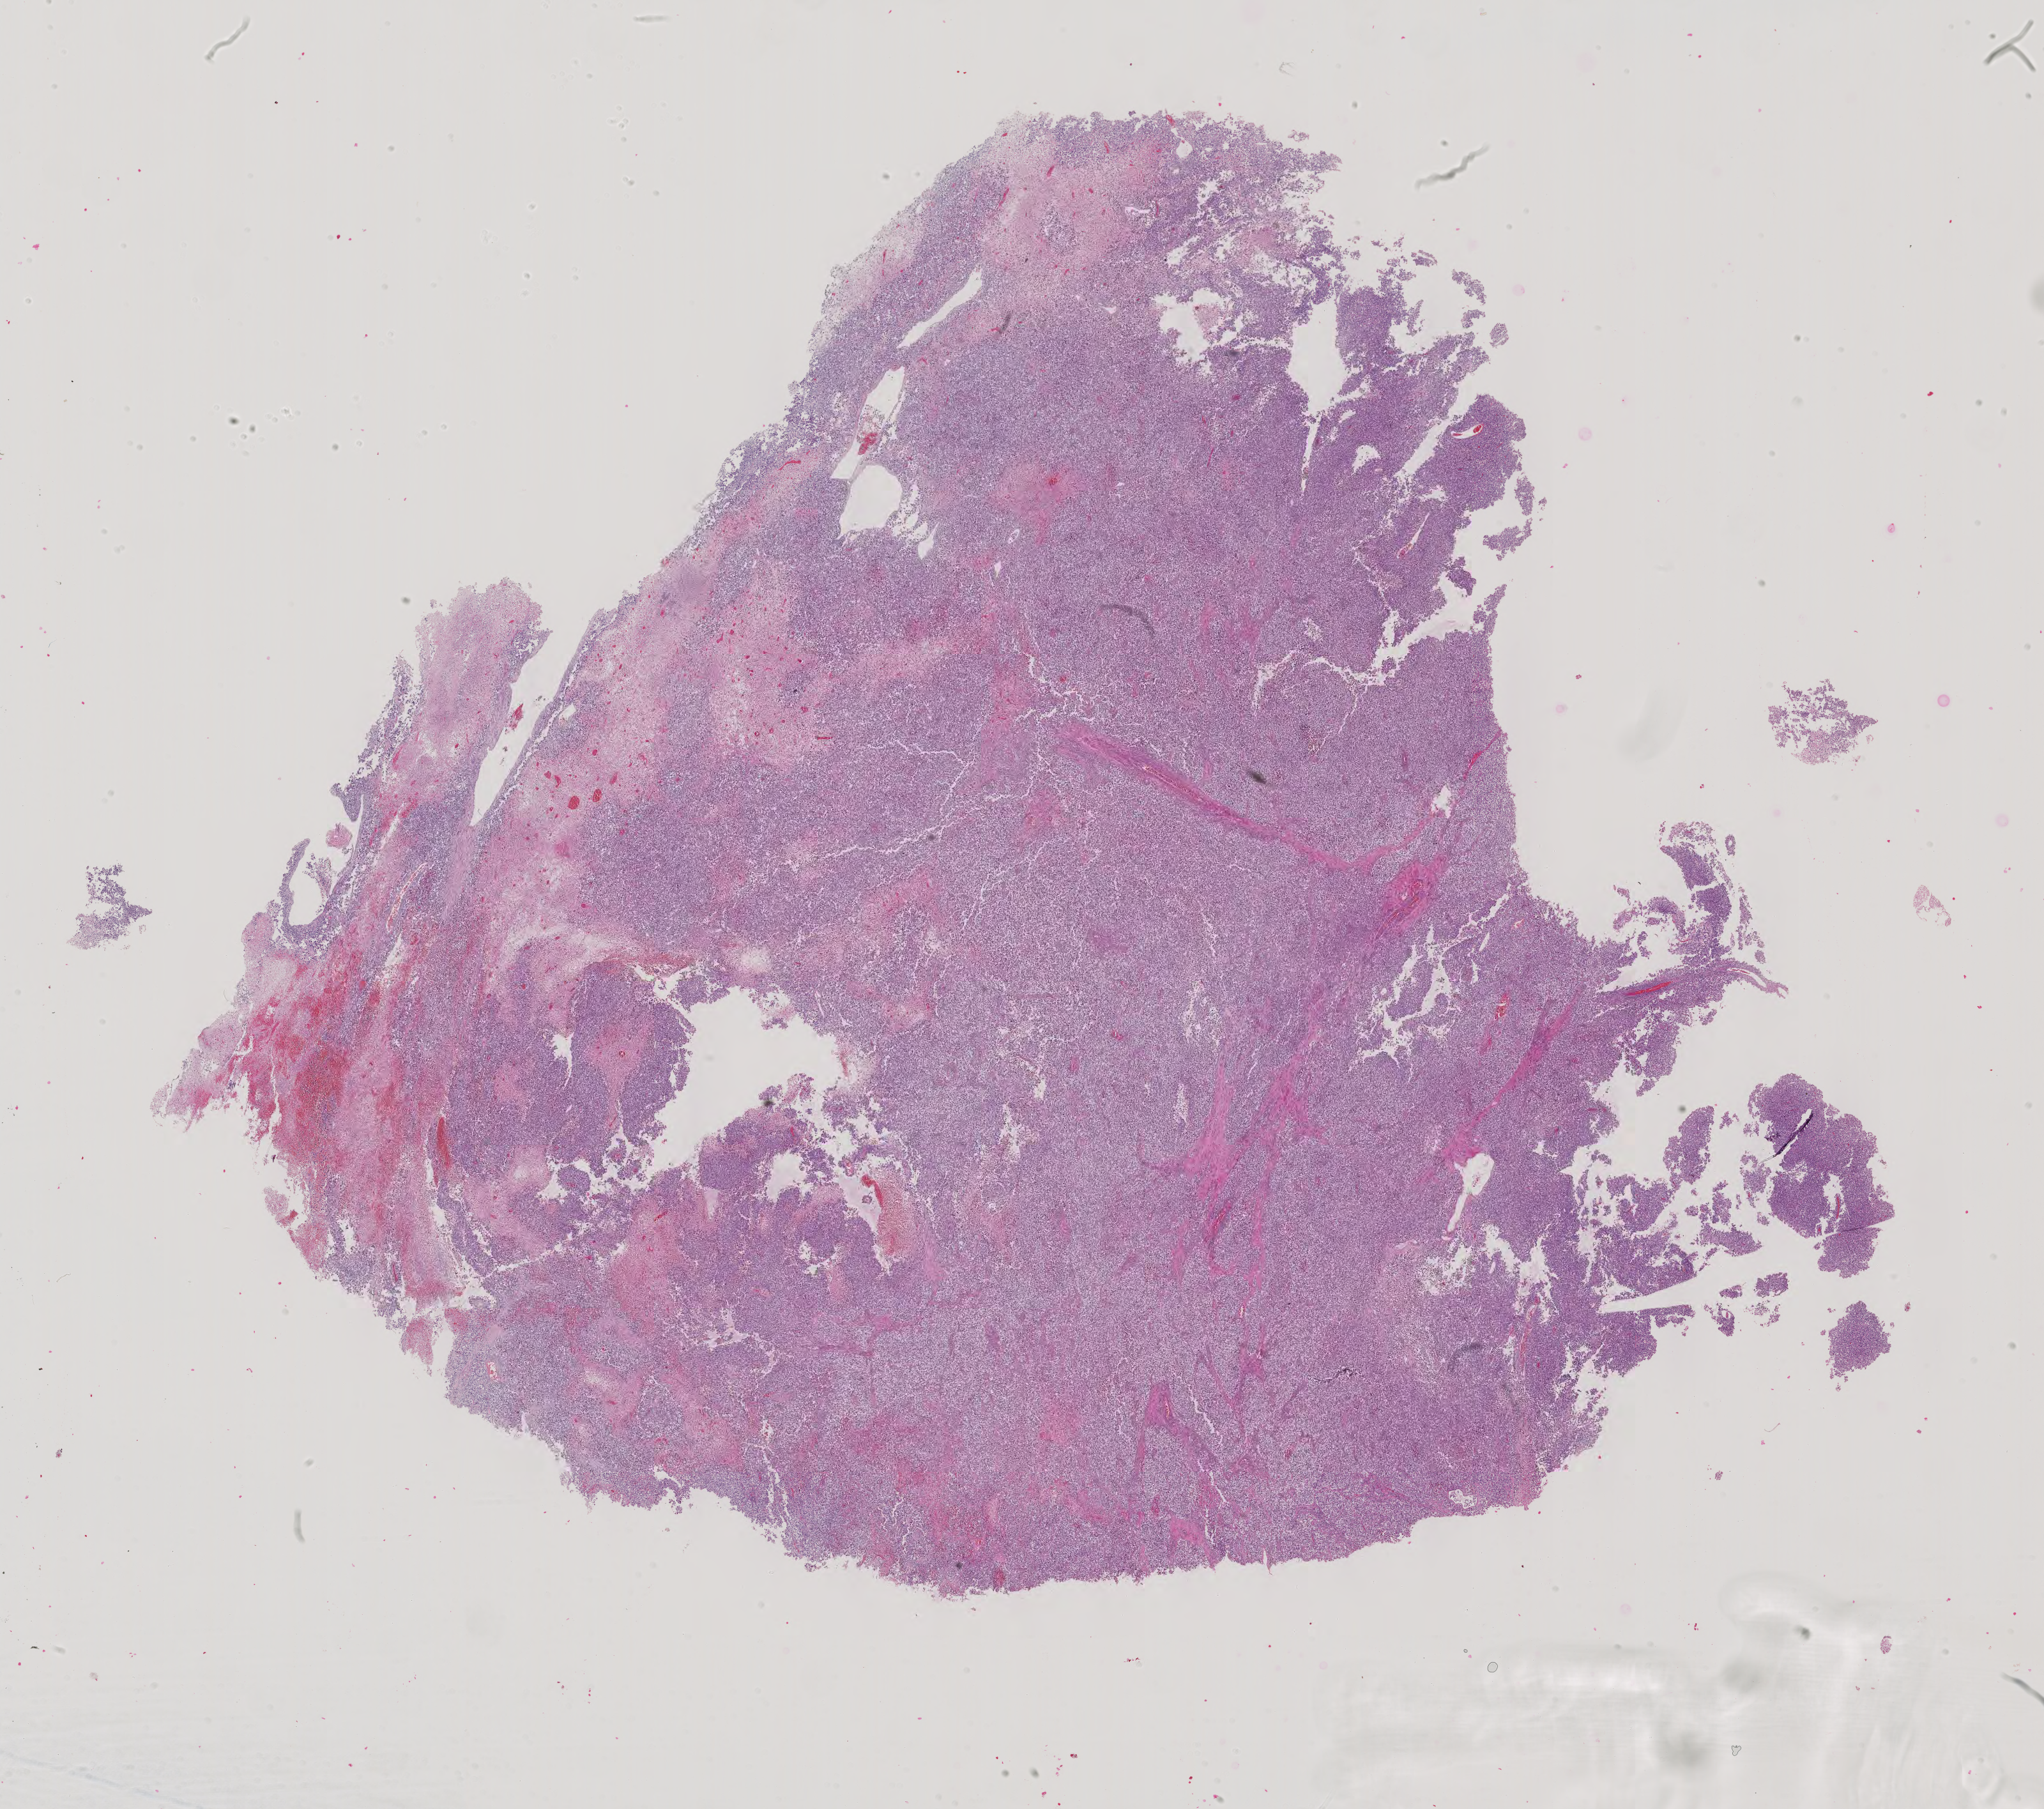
Digitized Hematoxylin and eosin (H&E) stained tissue section (whole slide) — whole scanned area (about 23.3 x 20.6 mm, acquisition: 40x scan) shown as a low-resolution overview; formalin-fixed paraffin-embedded (FFPE) diagnostic section; testis, primary tumour sample. Male patient; age at initial diagnosis 45 years.
AJCC pathologic stage: IIIC (6th edition). Laterality: right. Pathologic diagnosis: Seminoma, NOS. TNM: T2 NX M0.